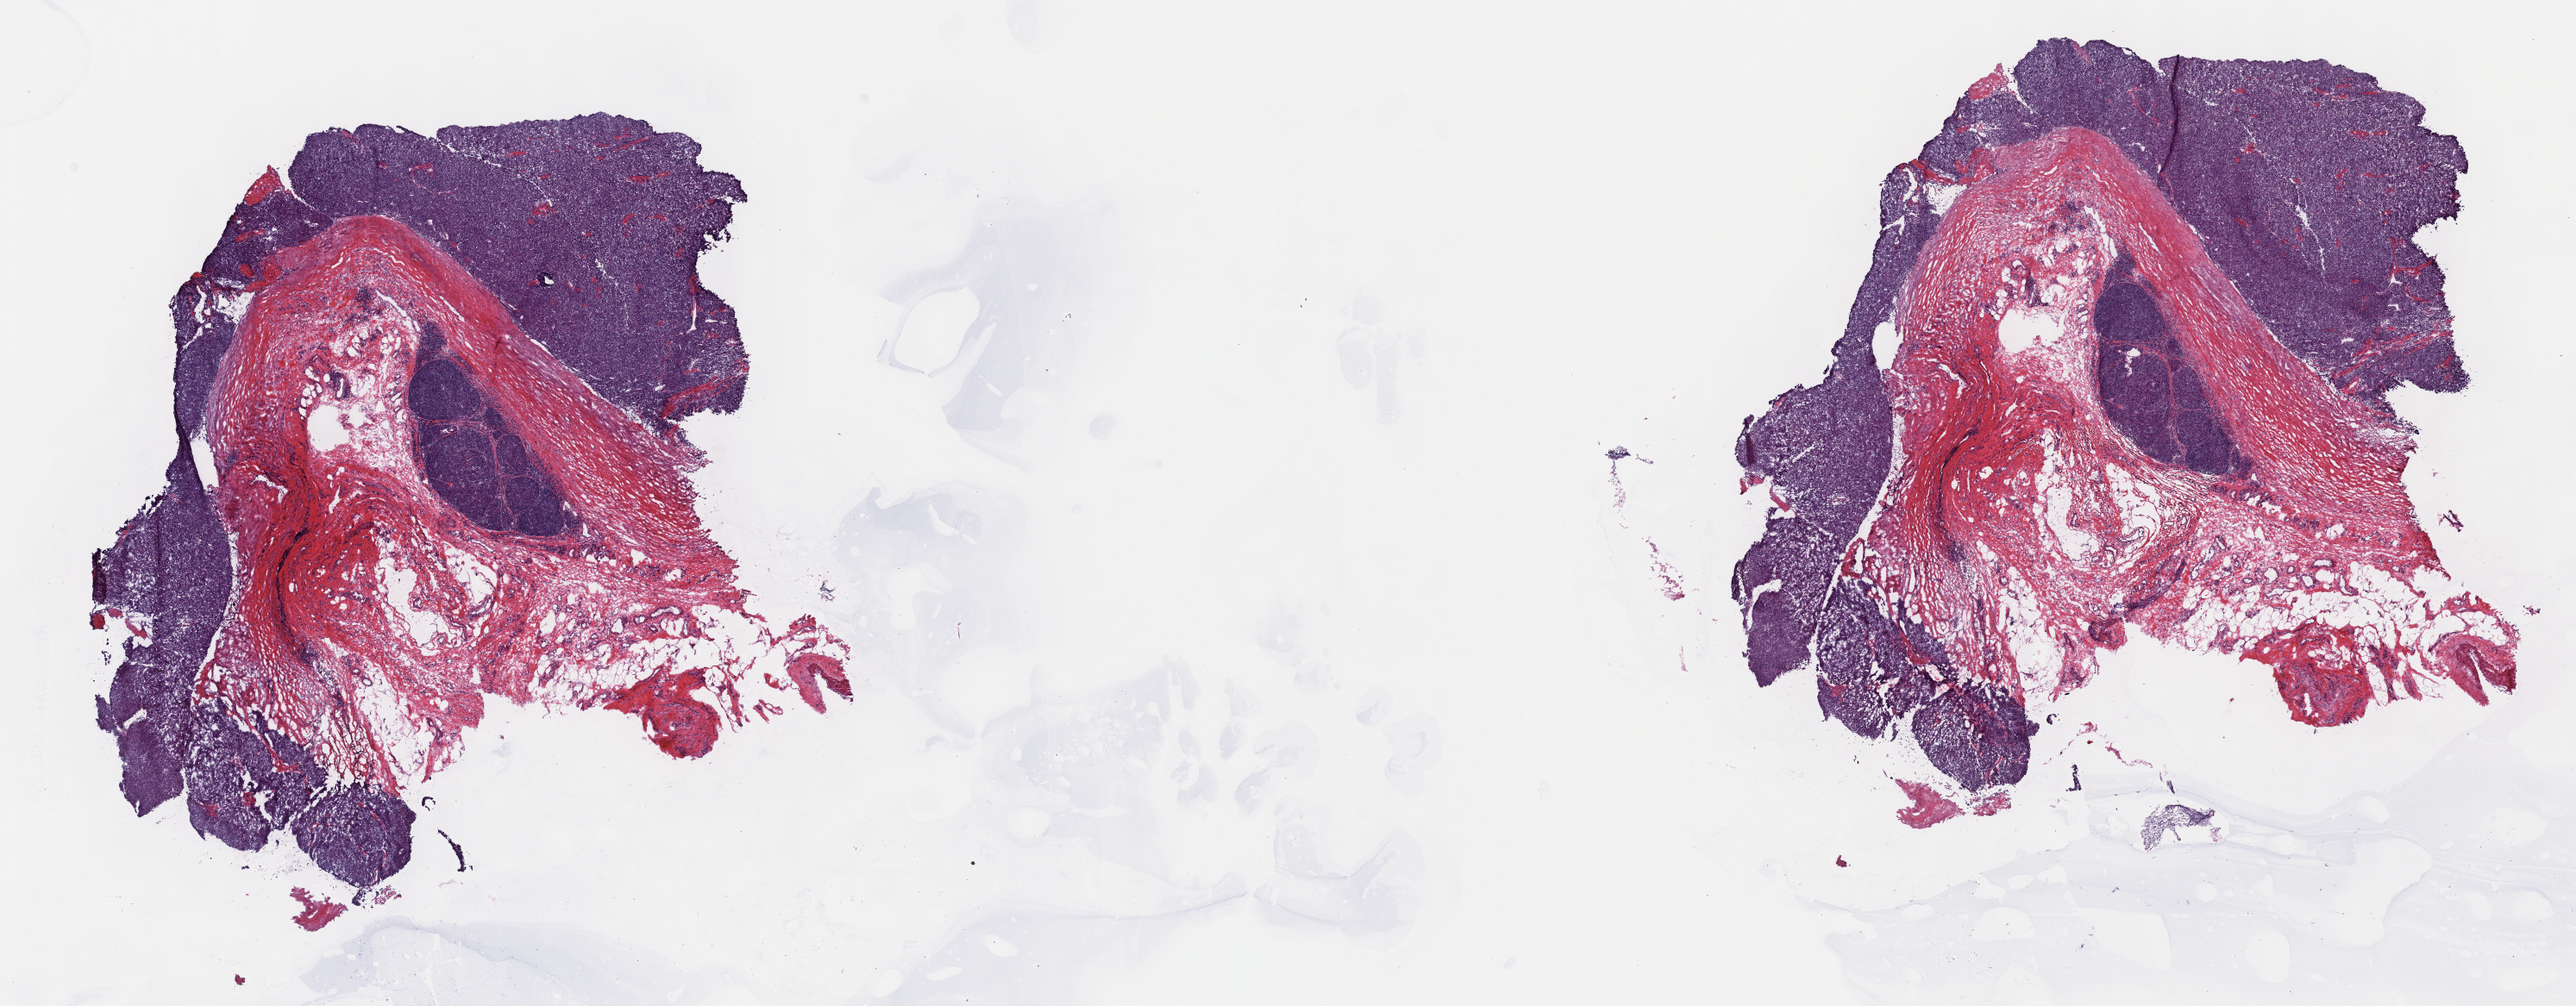
Digitized H&E tissue section (whole slide) — low-resolution overview of the scanned area, about 24.2 x 9.4 mm; frozen section from the top of the tissue portion; primary tumour sample from the thymus. Patient: female, age at initial diagnosis 58 years. Slide review estimates, as recorded: tumour cells 80%, tumour nuclei 80%, normal cells 0%, stromal cells 20%, necrosis 0%. Inflammatory infiltration, as recorded: lymphocyte infiltration 3%, monocyte infiltration 1%, neutrophil infiltration 2%.
* pathologic diagnosis: Thymoma, type AB, malignant